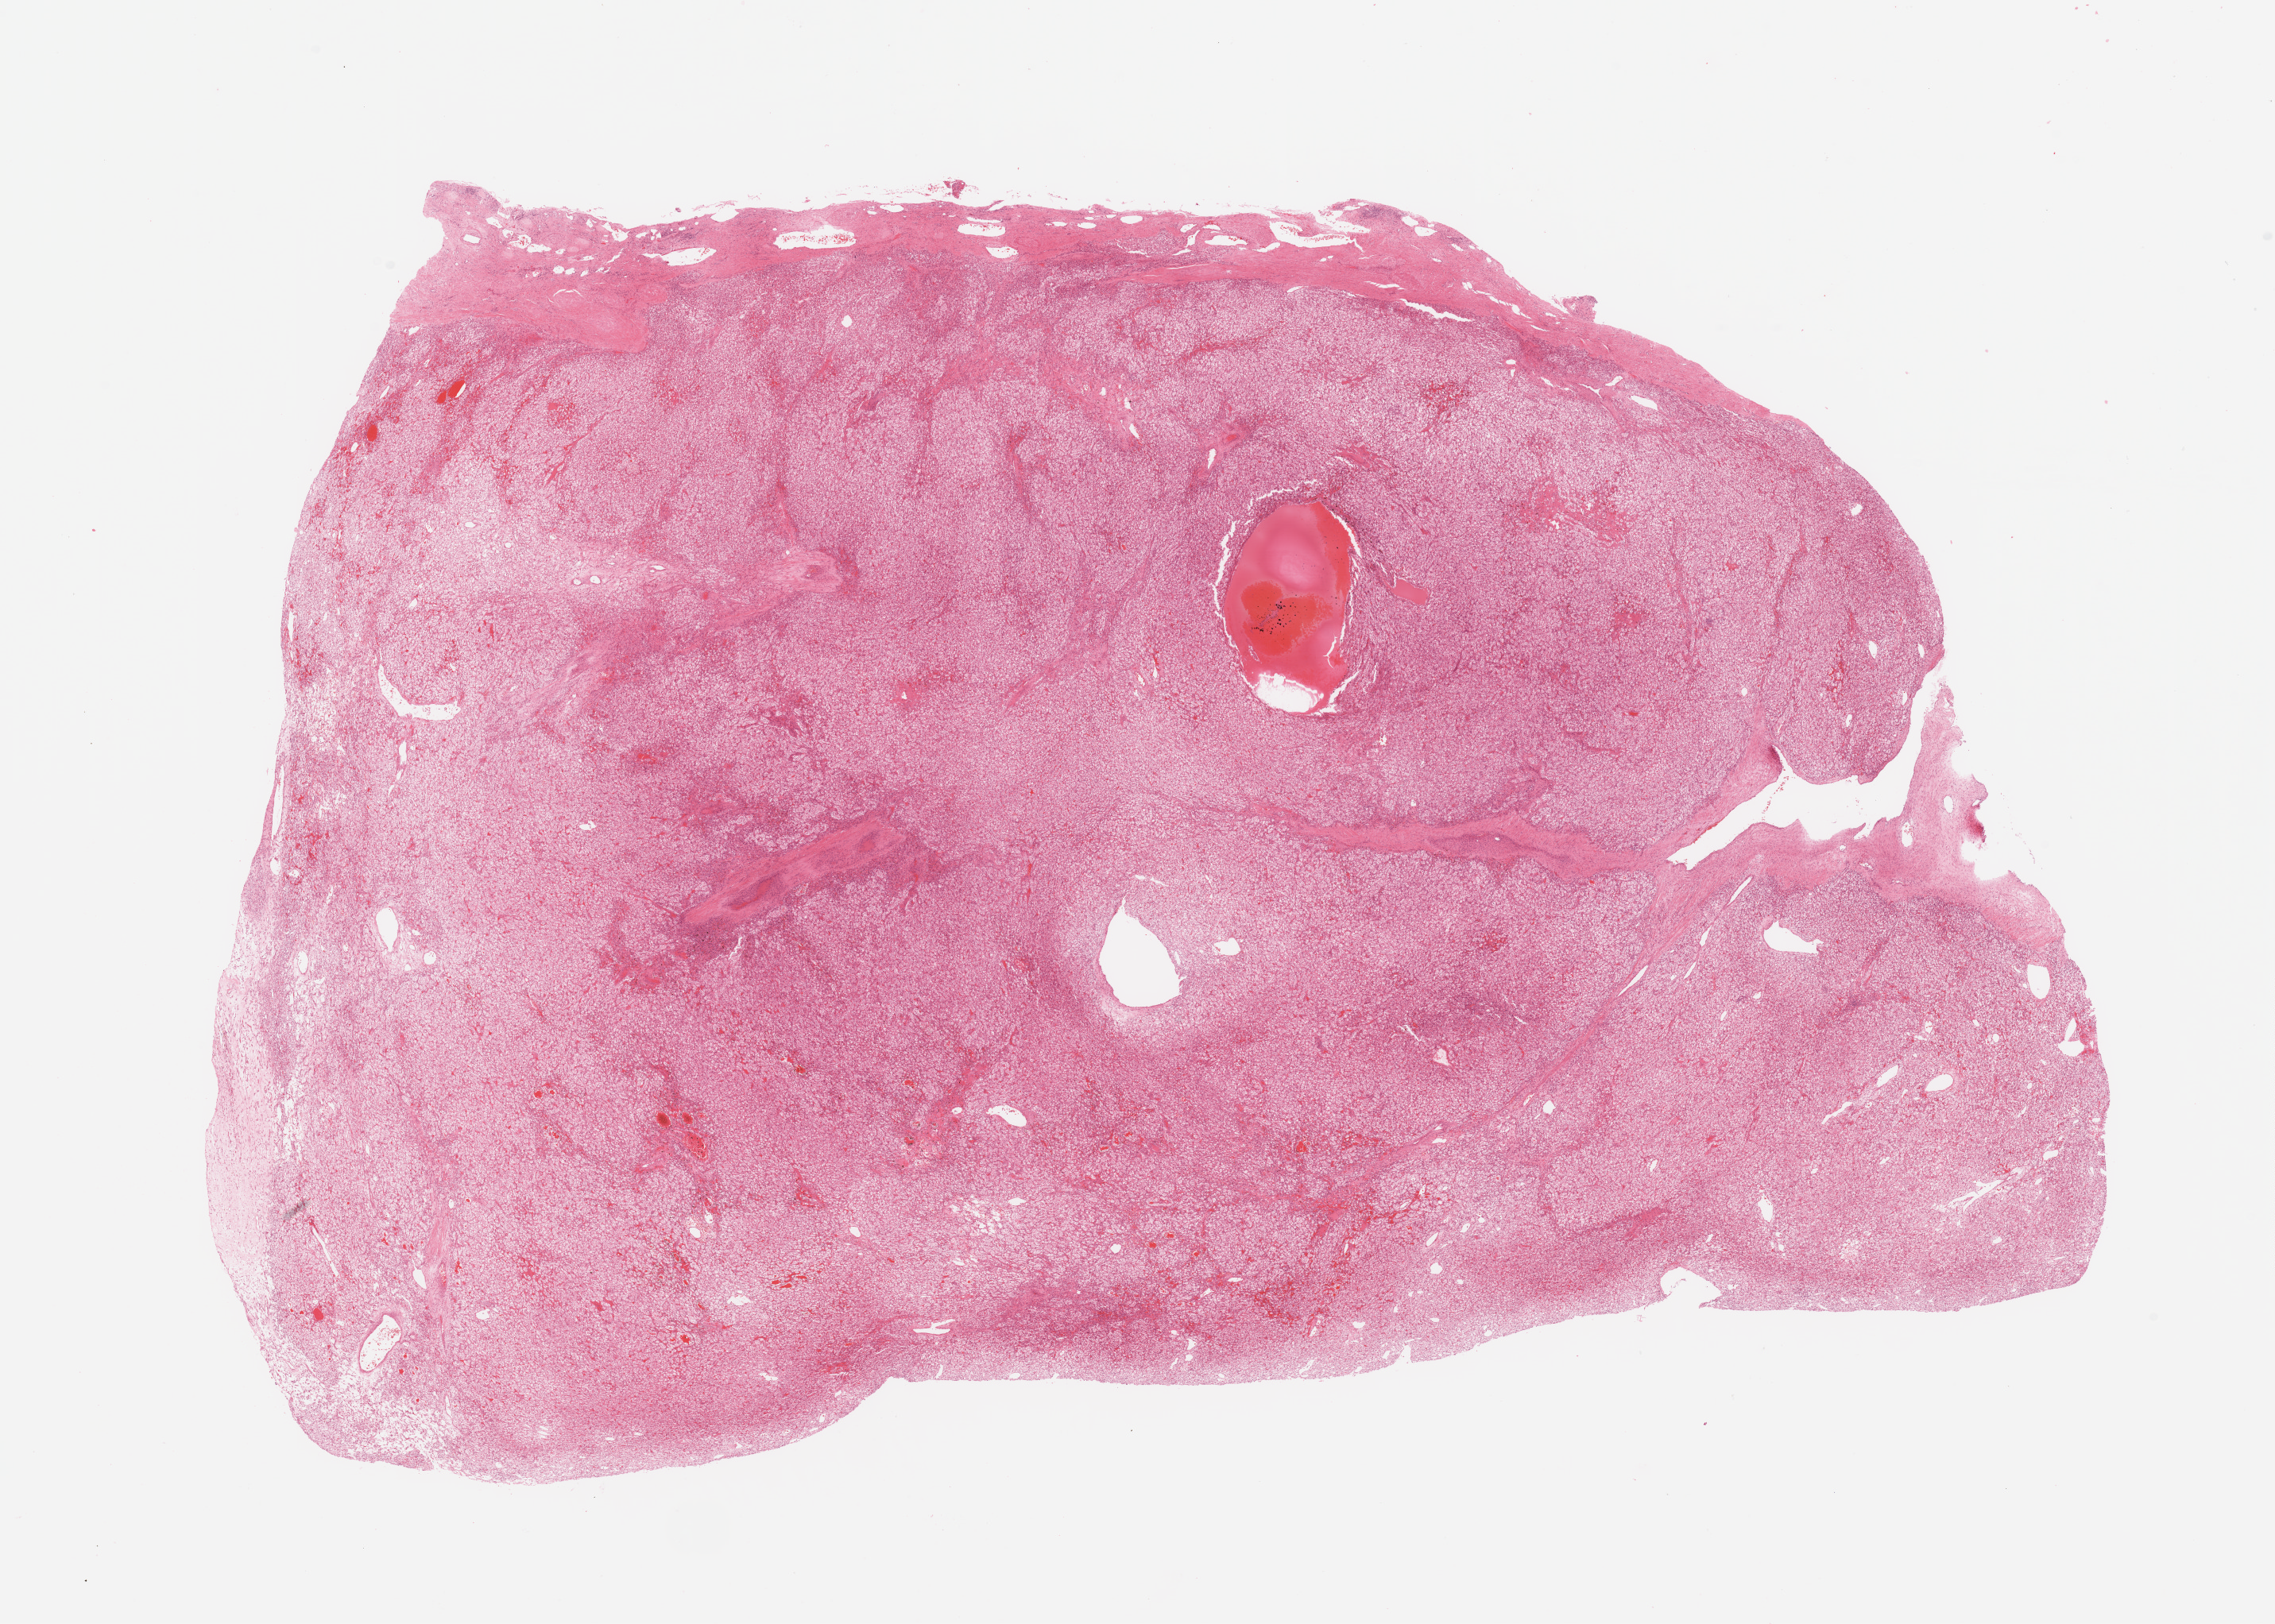
Digitized Hematoxylin and eosin (H&E) stained tissue section (whole slide) — shown as a low-resolution overview of the whole scanned area (about 22.6 x 16.2 mm, from a 20x scan). Tumour tissue sample, sampled site: kidney. 41-year-old female patient. Histologic grade: G2 (moderately differentiated). Composition of this section per pathologist review: tumour nuclei 85%, necrosis 0%.
Diagnosis: Renal cell carcinoma, NOS. Primary tumour site (as recorded): lower pole.